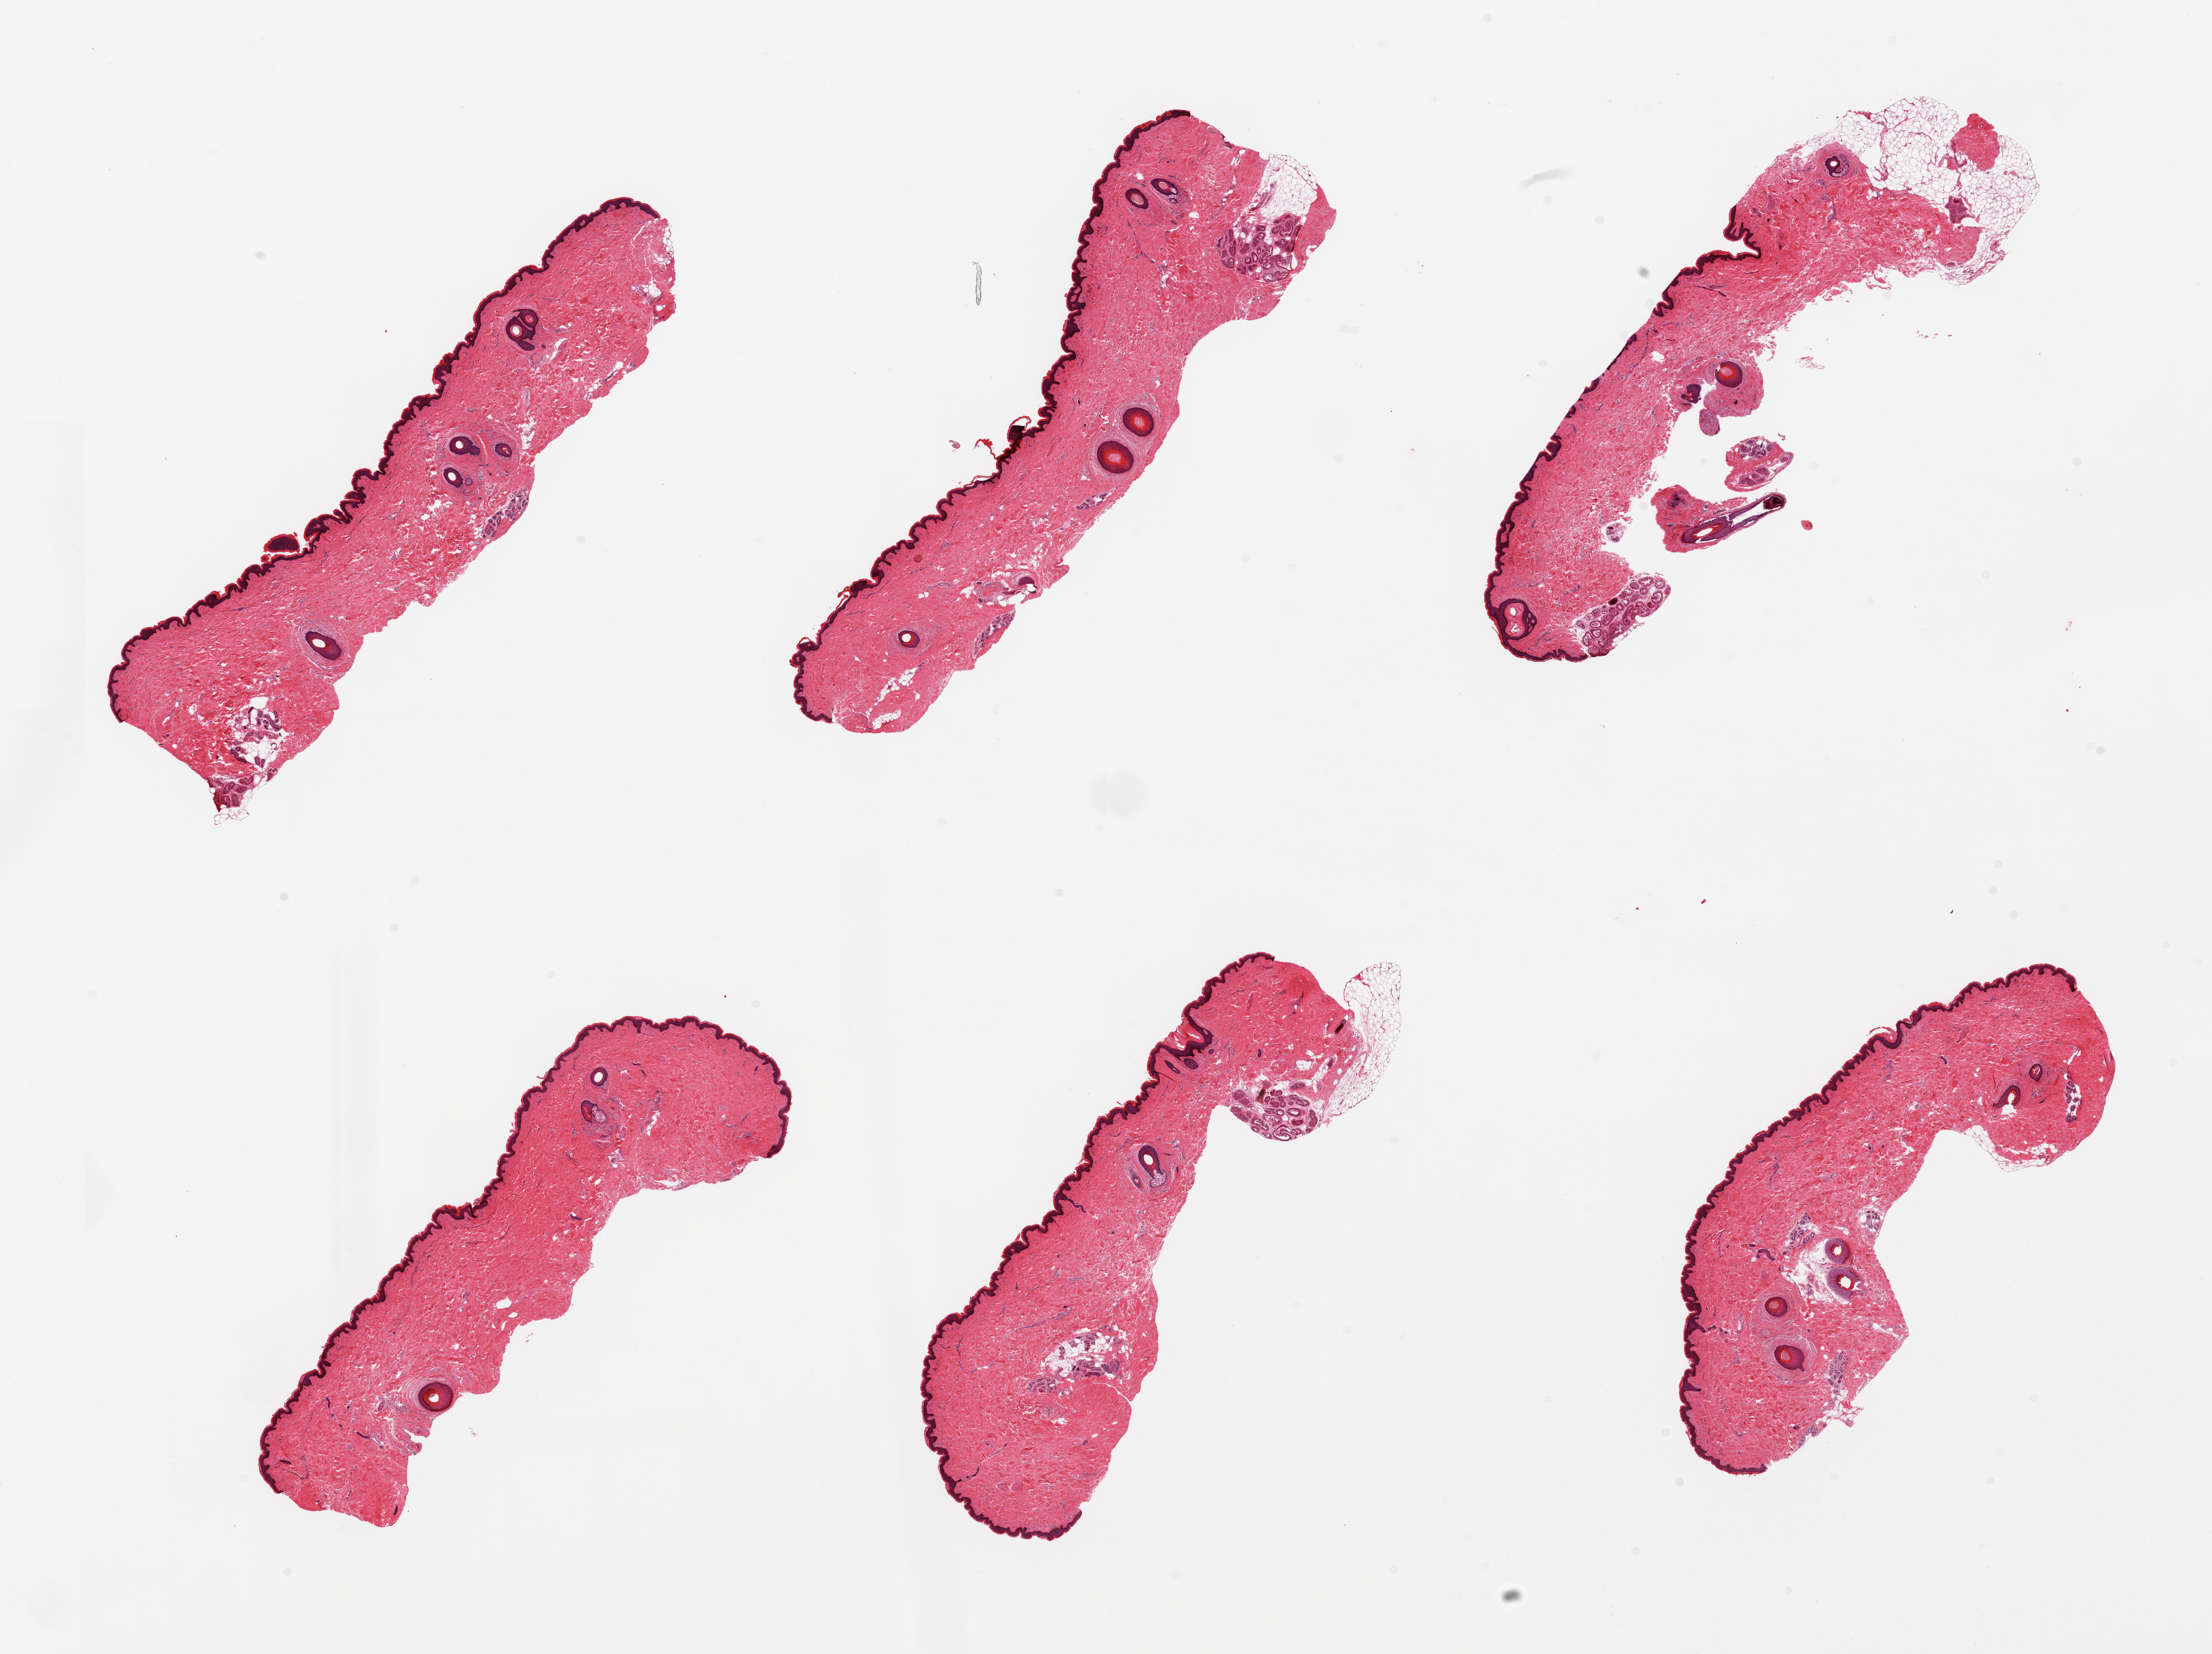
Whole-slide image, hematoxylin and eosin (H&E) stain, brightfield — whole scanned area (about 25.6 x 19.1 mm) shown as a low-resolution overview; PAXgene-fixed paraffin-embedded (PFPE) section; target tissue: skin of suprapubic region; donor tissue sample. Donor sex: female.
Pathologist's review note for this sample: 6 pieces; hair bearing skin, few pieces with 5-10% external fat.